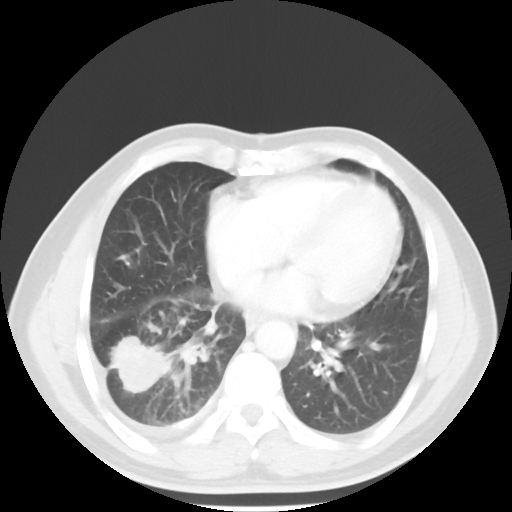
Chest CT, one axial slice; slice 21 of 56 in the series (ordered by position); reconstruction kernel STANDARD; 120 kVp; lung window (W 1500 / L -600 HU); 5 mm slice thickness; 512 × 512 image matrix. Patient: male, 56 years. From the clinical record (not read from this slice): clinical TNM (as recorded): T2 N3 M1.
Annotated regions visible in this slice (bounding box drawn by a radiologist):
- lung tumour (recorded histology: adenocarcinoma): box from (x=112, y=333) to (x=175, y=401) px